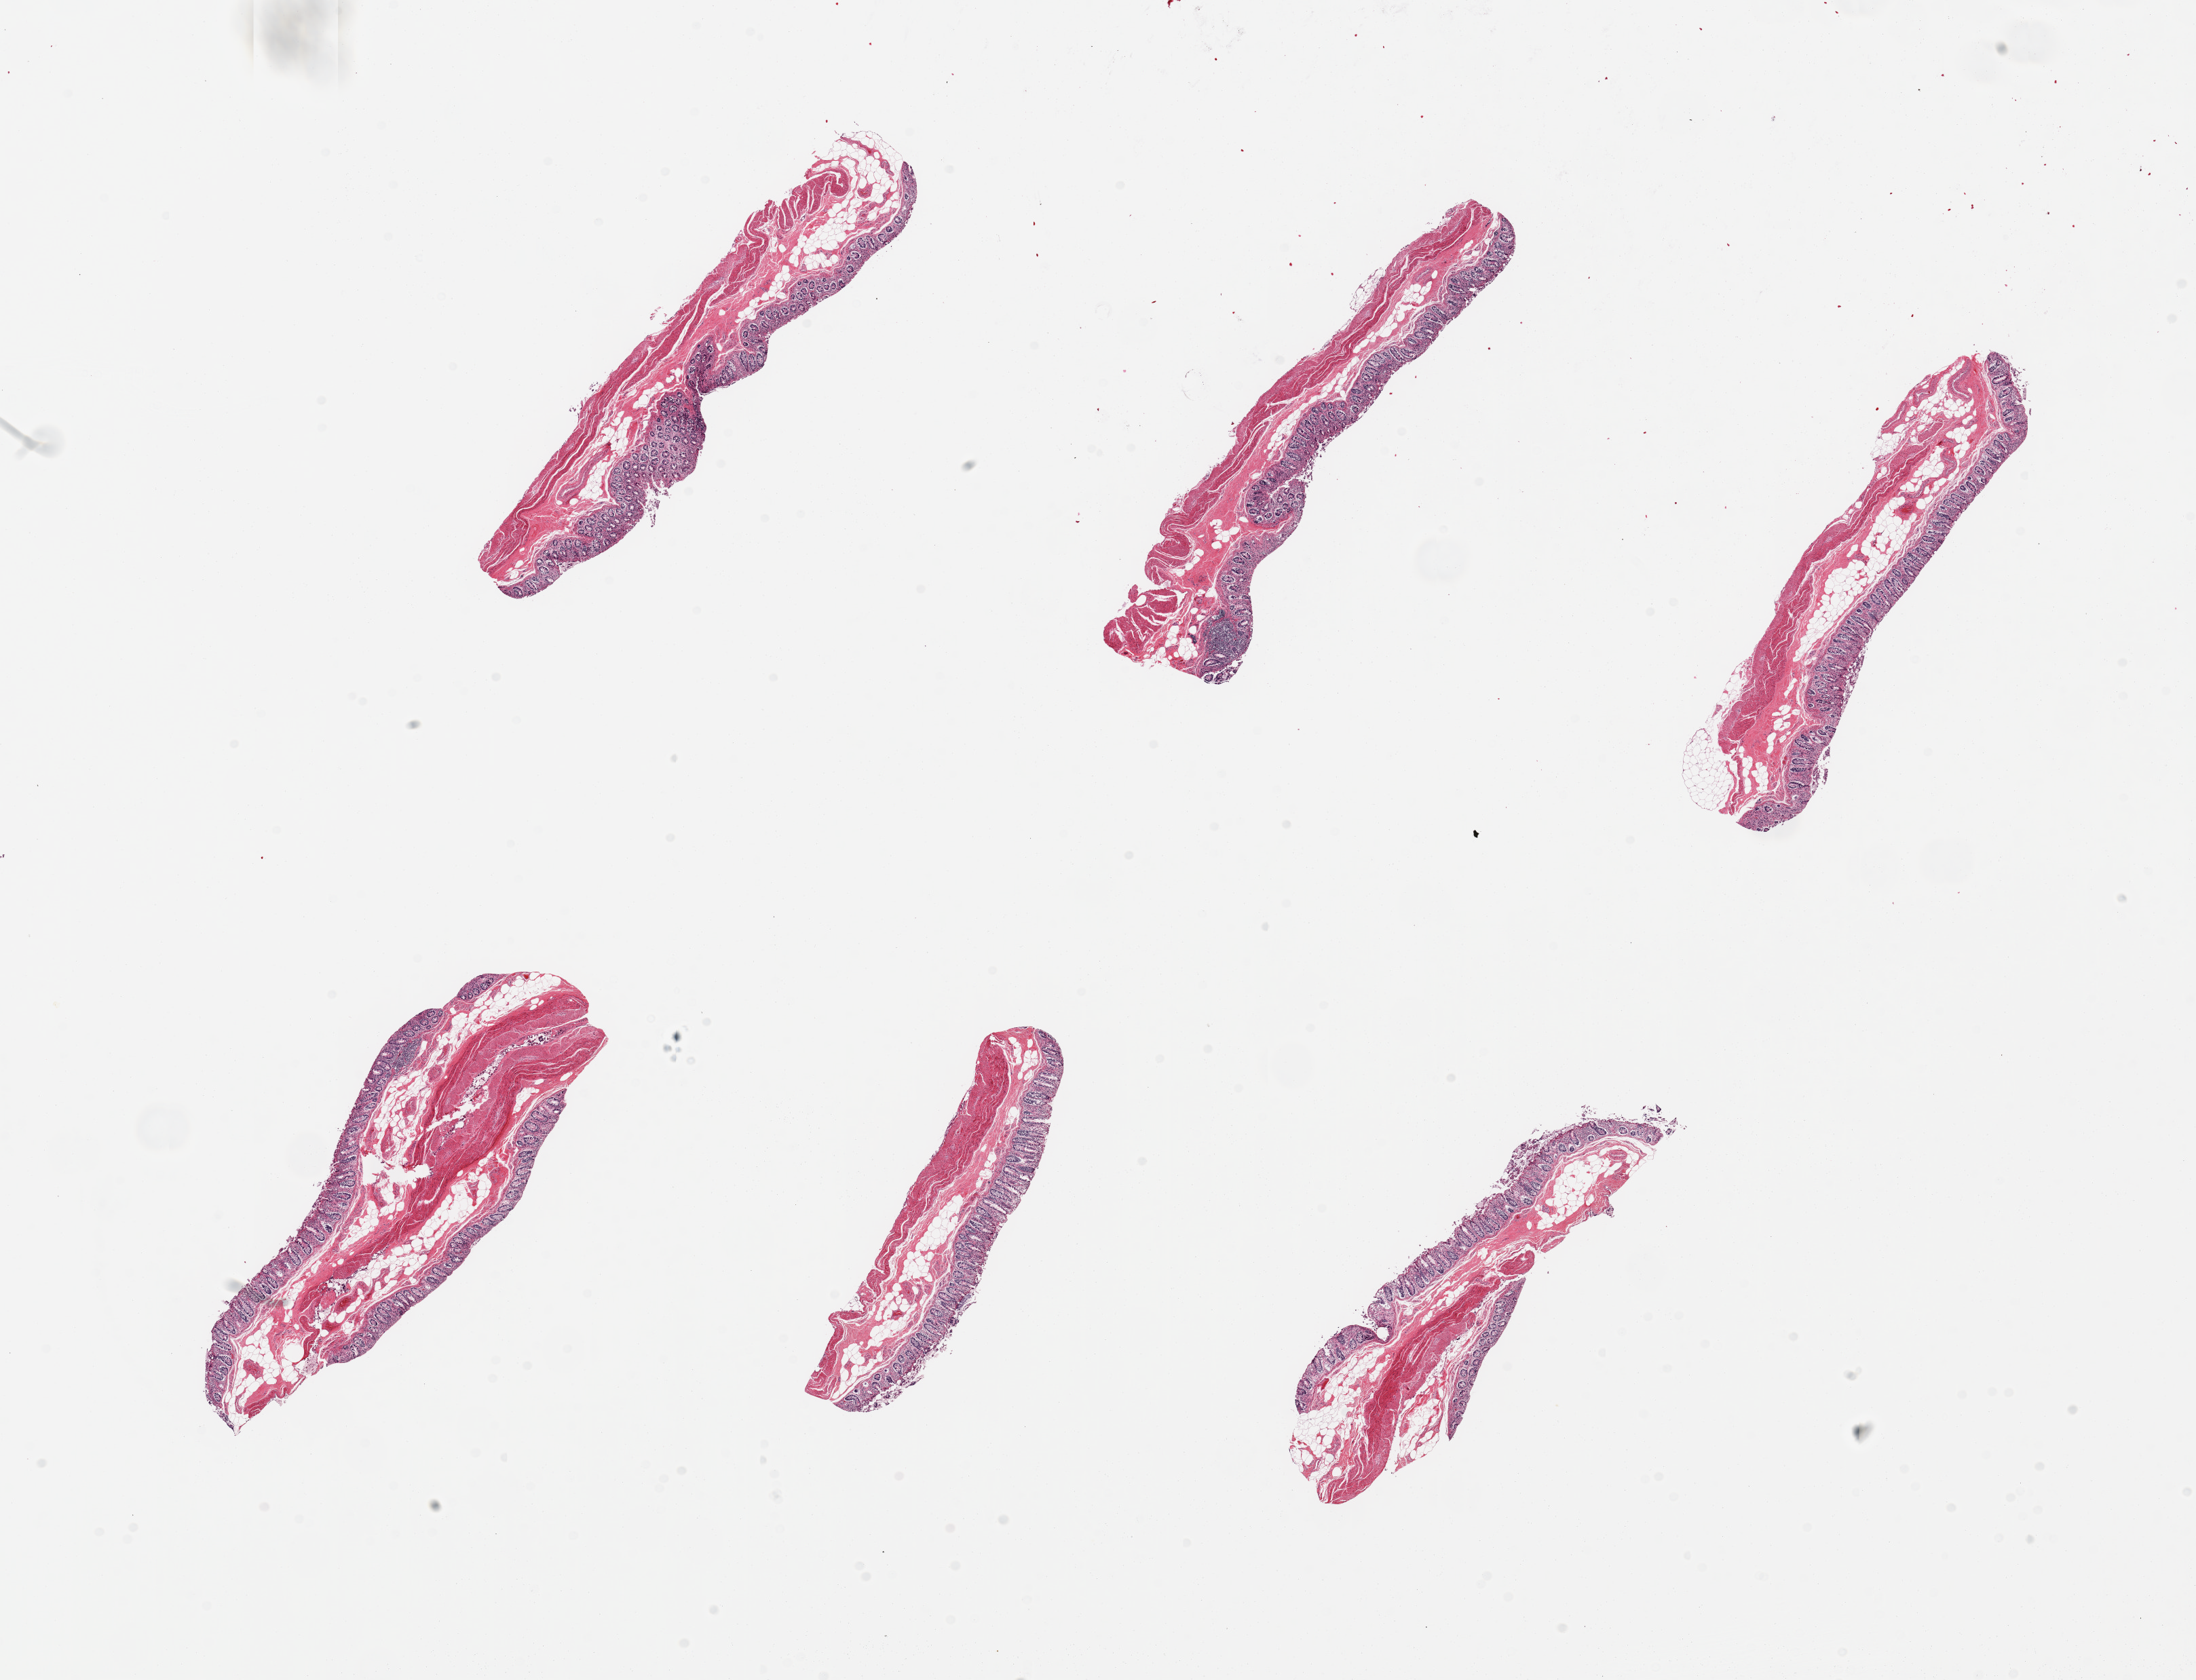
Whole-slide image, hematoxylin and eosin (H&E) stain — a low-resolution overview of the entire scanned area, about 25.6 x 19.6 mm (slide scanned at 20x). PAXgene-fixed paraffin-embedded (PFPE) section. Sampled site (target tissue): transverse colon. Donor tissue sample. Donor sex: male.
Reviewer comment on this tissue sample: 6 pieces, mucosa up to ~0.7mm, ~40-50% thickness; glandular component of mucosa moderately markedly autolyzed.